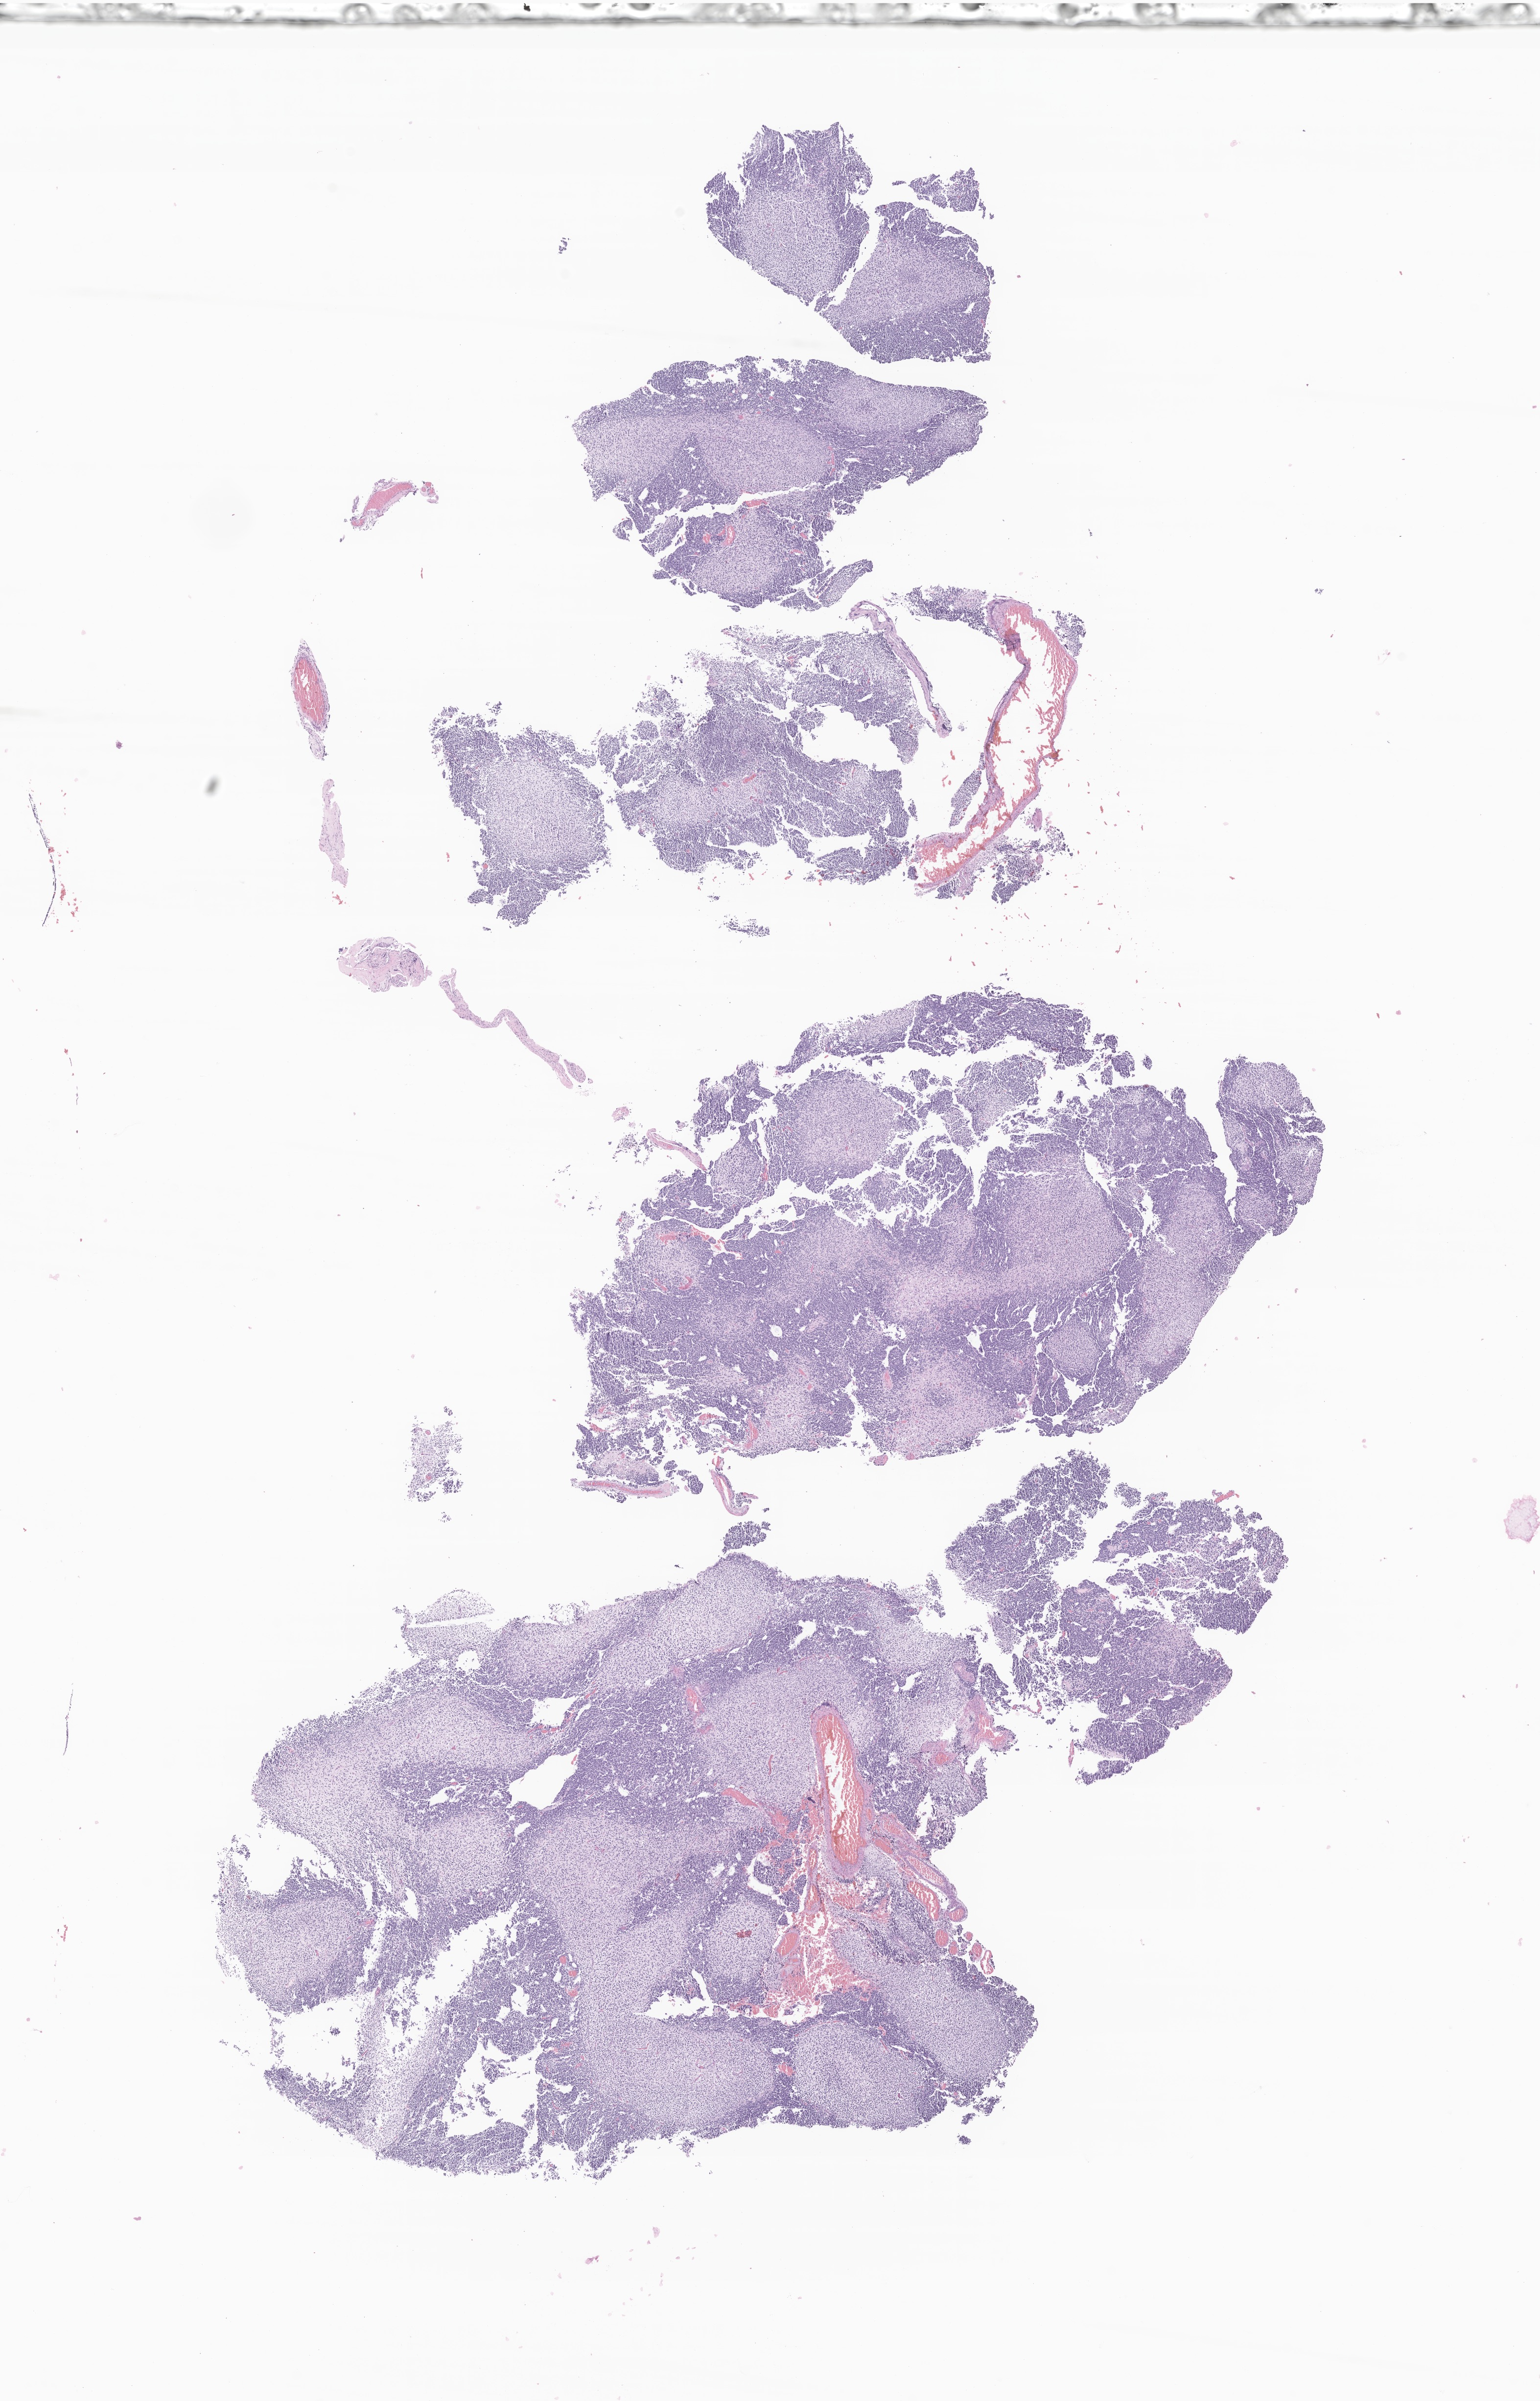
Whole-slide image, haematoxylin and eosin stain of tumor tissue from the brain, a low-resolution overview of the entire scanned area, about 13.3 x 20.7 mm. Formalin-fixed, paraffin-embedded (FFPE) tissue. Patient female; age 40 months.
Diagnosis (ICD-O-3 morphology term): Medulloblastoma, NOS.